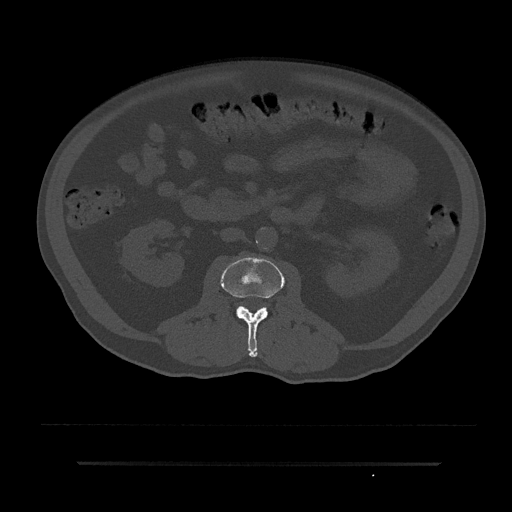
CT including the spine, one axial slice. Slice 56 of 797 in the series (ordered by position). Reconstruction kernel Br40s/3. 120 kVp. Bone window (W 1800 / L 400 HU). 512 × 512 image matrix. Male patient, age 59 years. From the clinical record (not read from this slice): primary cancer: bile ducts.
Annotated regions visible in this slice (semi-automatically segmented with operator editing):
- L2 vertebra: box from (x=221, y=256) to (x=285, y=357) px